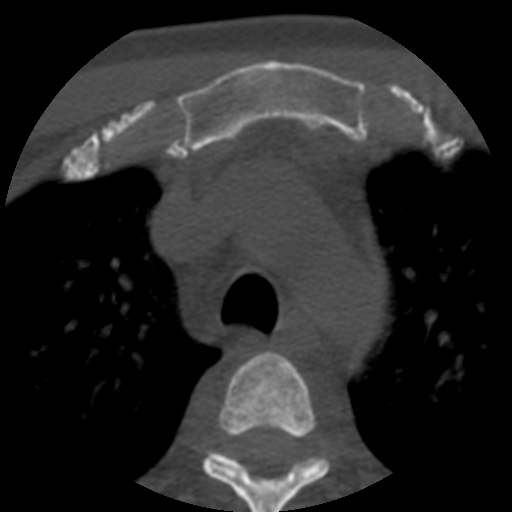
CT including the spine, one axial slice; position 410 of 508 along the scan axis; 120 kVp; bone window (W 1800 / L 400 HU); 512 × 512 image matrix, field of view 160 × 160 mm. Patient age 57 years. From the clinical record (not read from this slice): primary cancer: prostate.
Annotated regions visible in this slice (semi-automatically segmented with operator editing):
- T3 vertebra: box from (x=202, y=351) to (x=329, y=512) px
- T4 vertebra: (x=220, y=453)–(x=321, y=471)